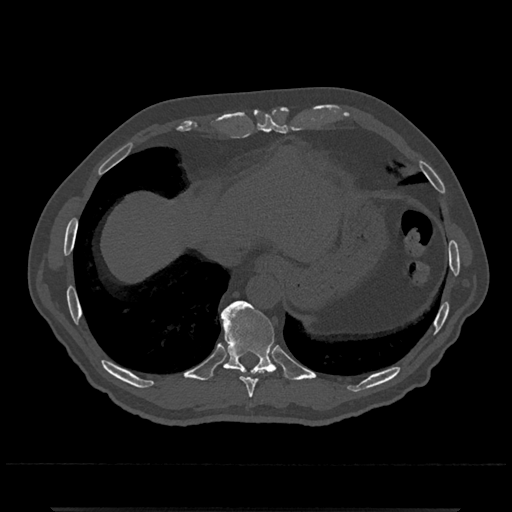
CT including the spine, one axial slice. Position 579 of 797 along the scan axis. Reconstruction kernel Br40s/3. Bone window (W 1800 / L 400 HU). 512 × 512 image matrix, field of view 393 × 393 mm. Male patient, age 67 years. Case-level facts recorded for this patient, not image findings: primary cancer: prostate.
Structures marked on this image (semi-automatic segmentation, software-assisted and operator-edited):
- T10 vertebra: box from (x=221, y=301) to (x=287, y=380) px
- T9 vertebra: (x=241, y=377)–(x=257, y=398)